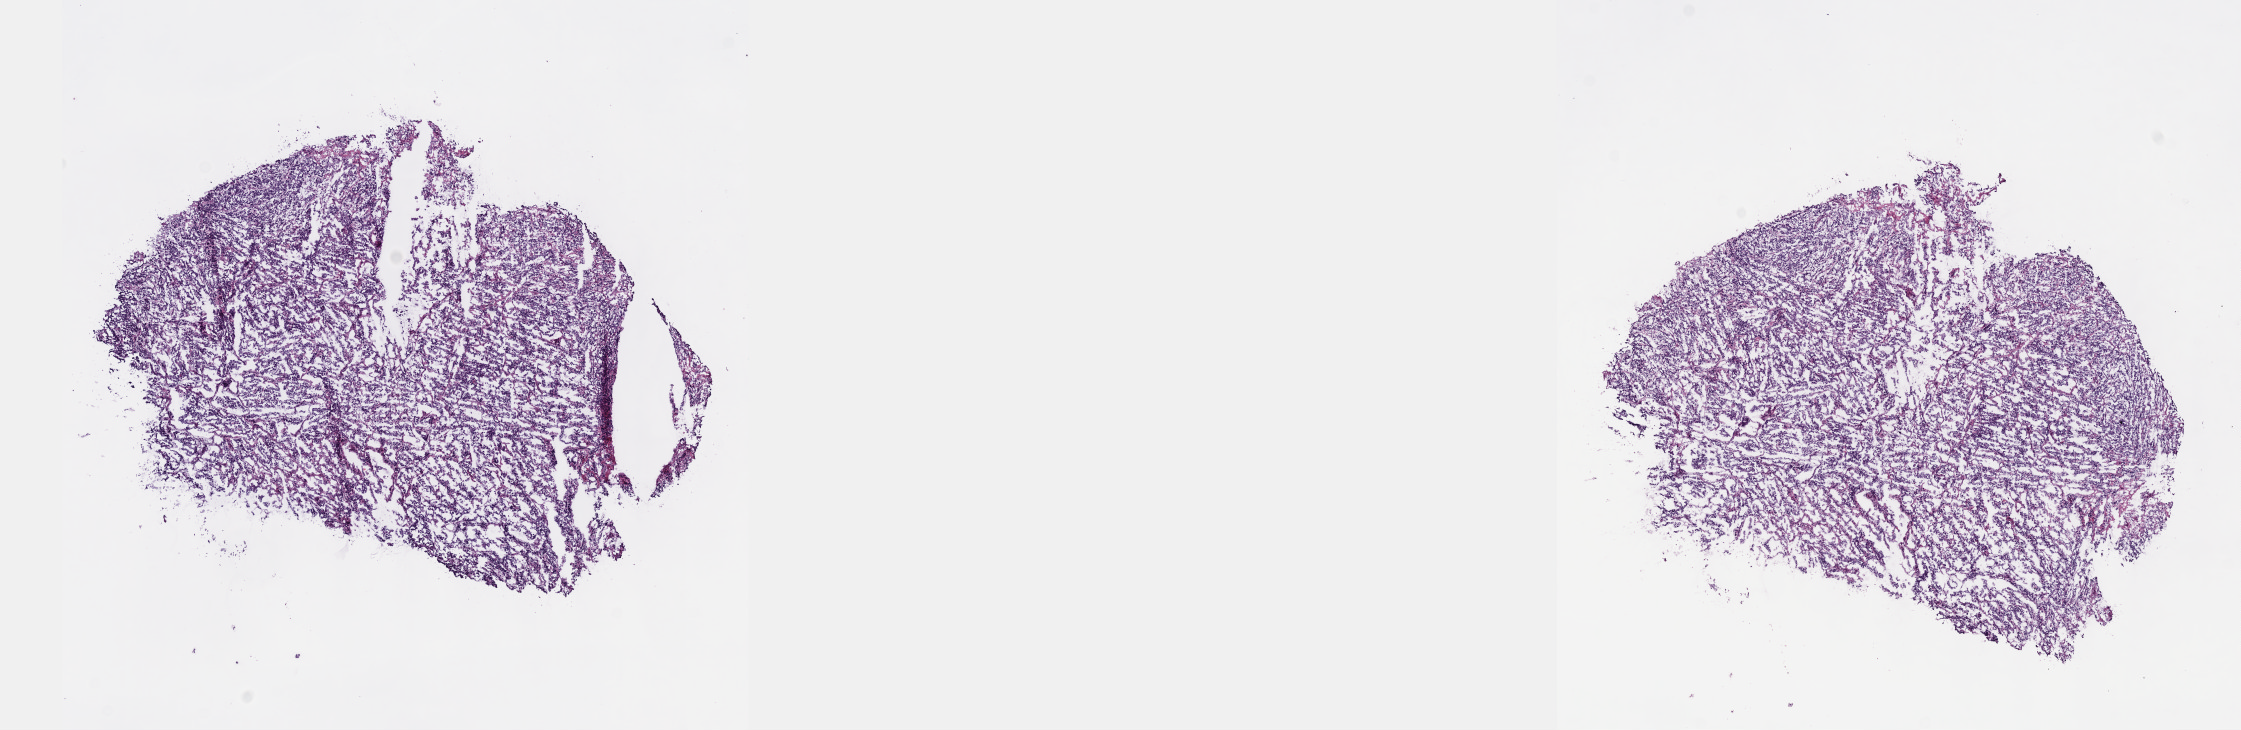
H&E-stained whole-slide image — whole scanned area (about 18.1 x 5.9 mm) shown as a low-resolution overview. Frozen section. Sample: primary tumour, testis. Male patient; age at initial diagnosis 27 years. Composition of this section per pathologist review: tumour cells 100%, tumour nuclei 85%.
Diagnosis: Embryonal carcinoma, NOS.